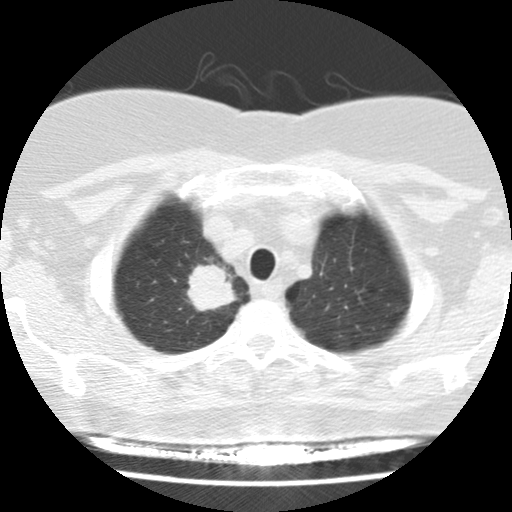
Low-dose screening chest CT, one axial slice; slice 130 of 148 in the series (ordered by position); reconstruction kernel STANDARD; 120 kVp; lung window (W 1500 / L -600 HU); 512 × 512 image matrix, field of view 281 × 281 mm.
Annotated regions visible in this slice (outlined manually by an expert reader):
- lesion 1 (tumor, upper lobe of right lung): bounding box <187,264,237,311> (left, top, right, bottom; pixels)